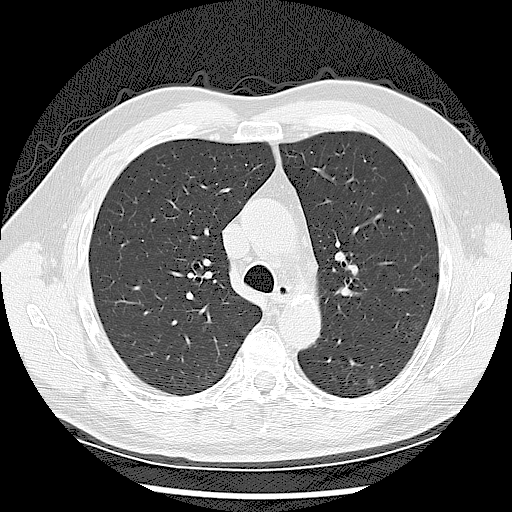
Low-dose screening chest CT, axial slice; baseline annual screen; lung window (W 1500 / L -600 HU); 2.5 mm slice thickness; slice 40 of 123 in the series. Male, age 65 years at enrolment.
• Lesion marked by an expert reader, bounding box [x1, y1, x2, y2] px = [358, 369, 388, 401].
• Screening reader's record for this exam (one nodule recorded; not confirmed to be the boxed lesion): non-calcified nodule or mass ≥4 mm, left lower lobe, 7 × 7 mm, smooth margins, soft tissue attenuation.
• Official screen result: positive, change unspecified: nodule(s) >= 4 mm or enlarging nodule(s), mass(es), or other non-specific abnormalities suspicious for lung cancer.
• Lung cancer was diagnosed 375 days after this screen: adenocarcinoma, NOS, left lower lobe, well differentiated (G1), stage IB (AJCC 6th edition), 10 mm at pathology.